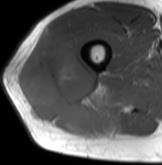
MRI of an extremity soft-tissue mass, one axial slice; slice 47 of 61 in the series (ordered by position); MR volume resampled by the dataset authors to the PET/CT grid (not the native acquisition matrix); 3.27 mm slice thickness; 162 × 165 image matrix. Male patient. From the clinical record (not read from this slice): histological type: poorly differentiated synovial sarcoma; grade: high; site of the primary tumour: right buttock.
Annotated regions visible in this slice (expert contour drawn on MRI and transferred to this co-registered scan by the dataset authors):
- gross tumour volume including surrounding oedema: bounding box (x1, y1, x2, y2) in pixels: (20, 31, 113, 133)
- gross tumour volume (mass): (20, 31, 113, 133)